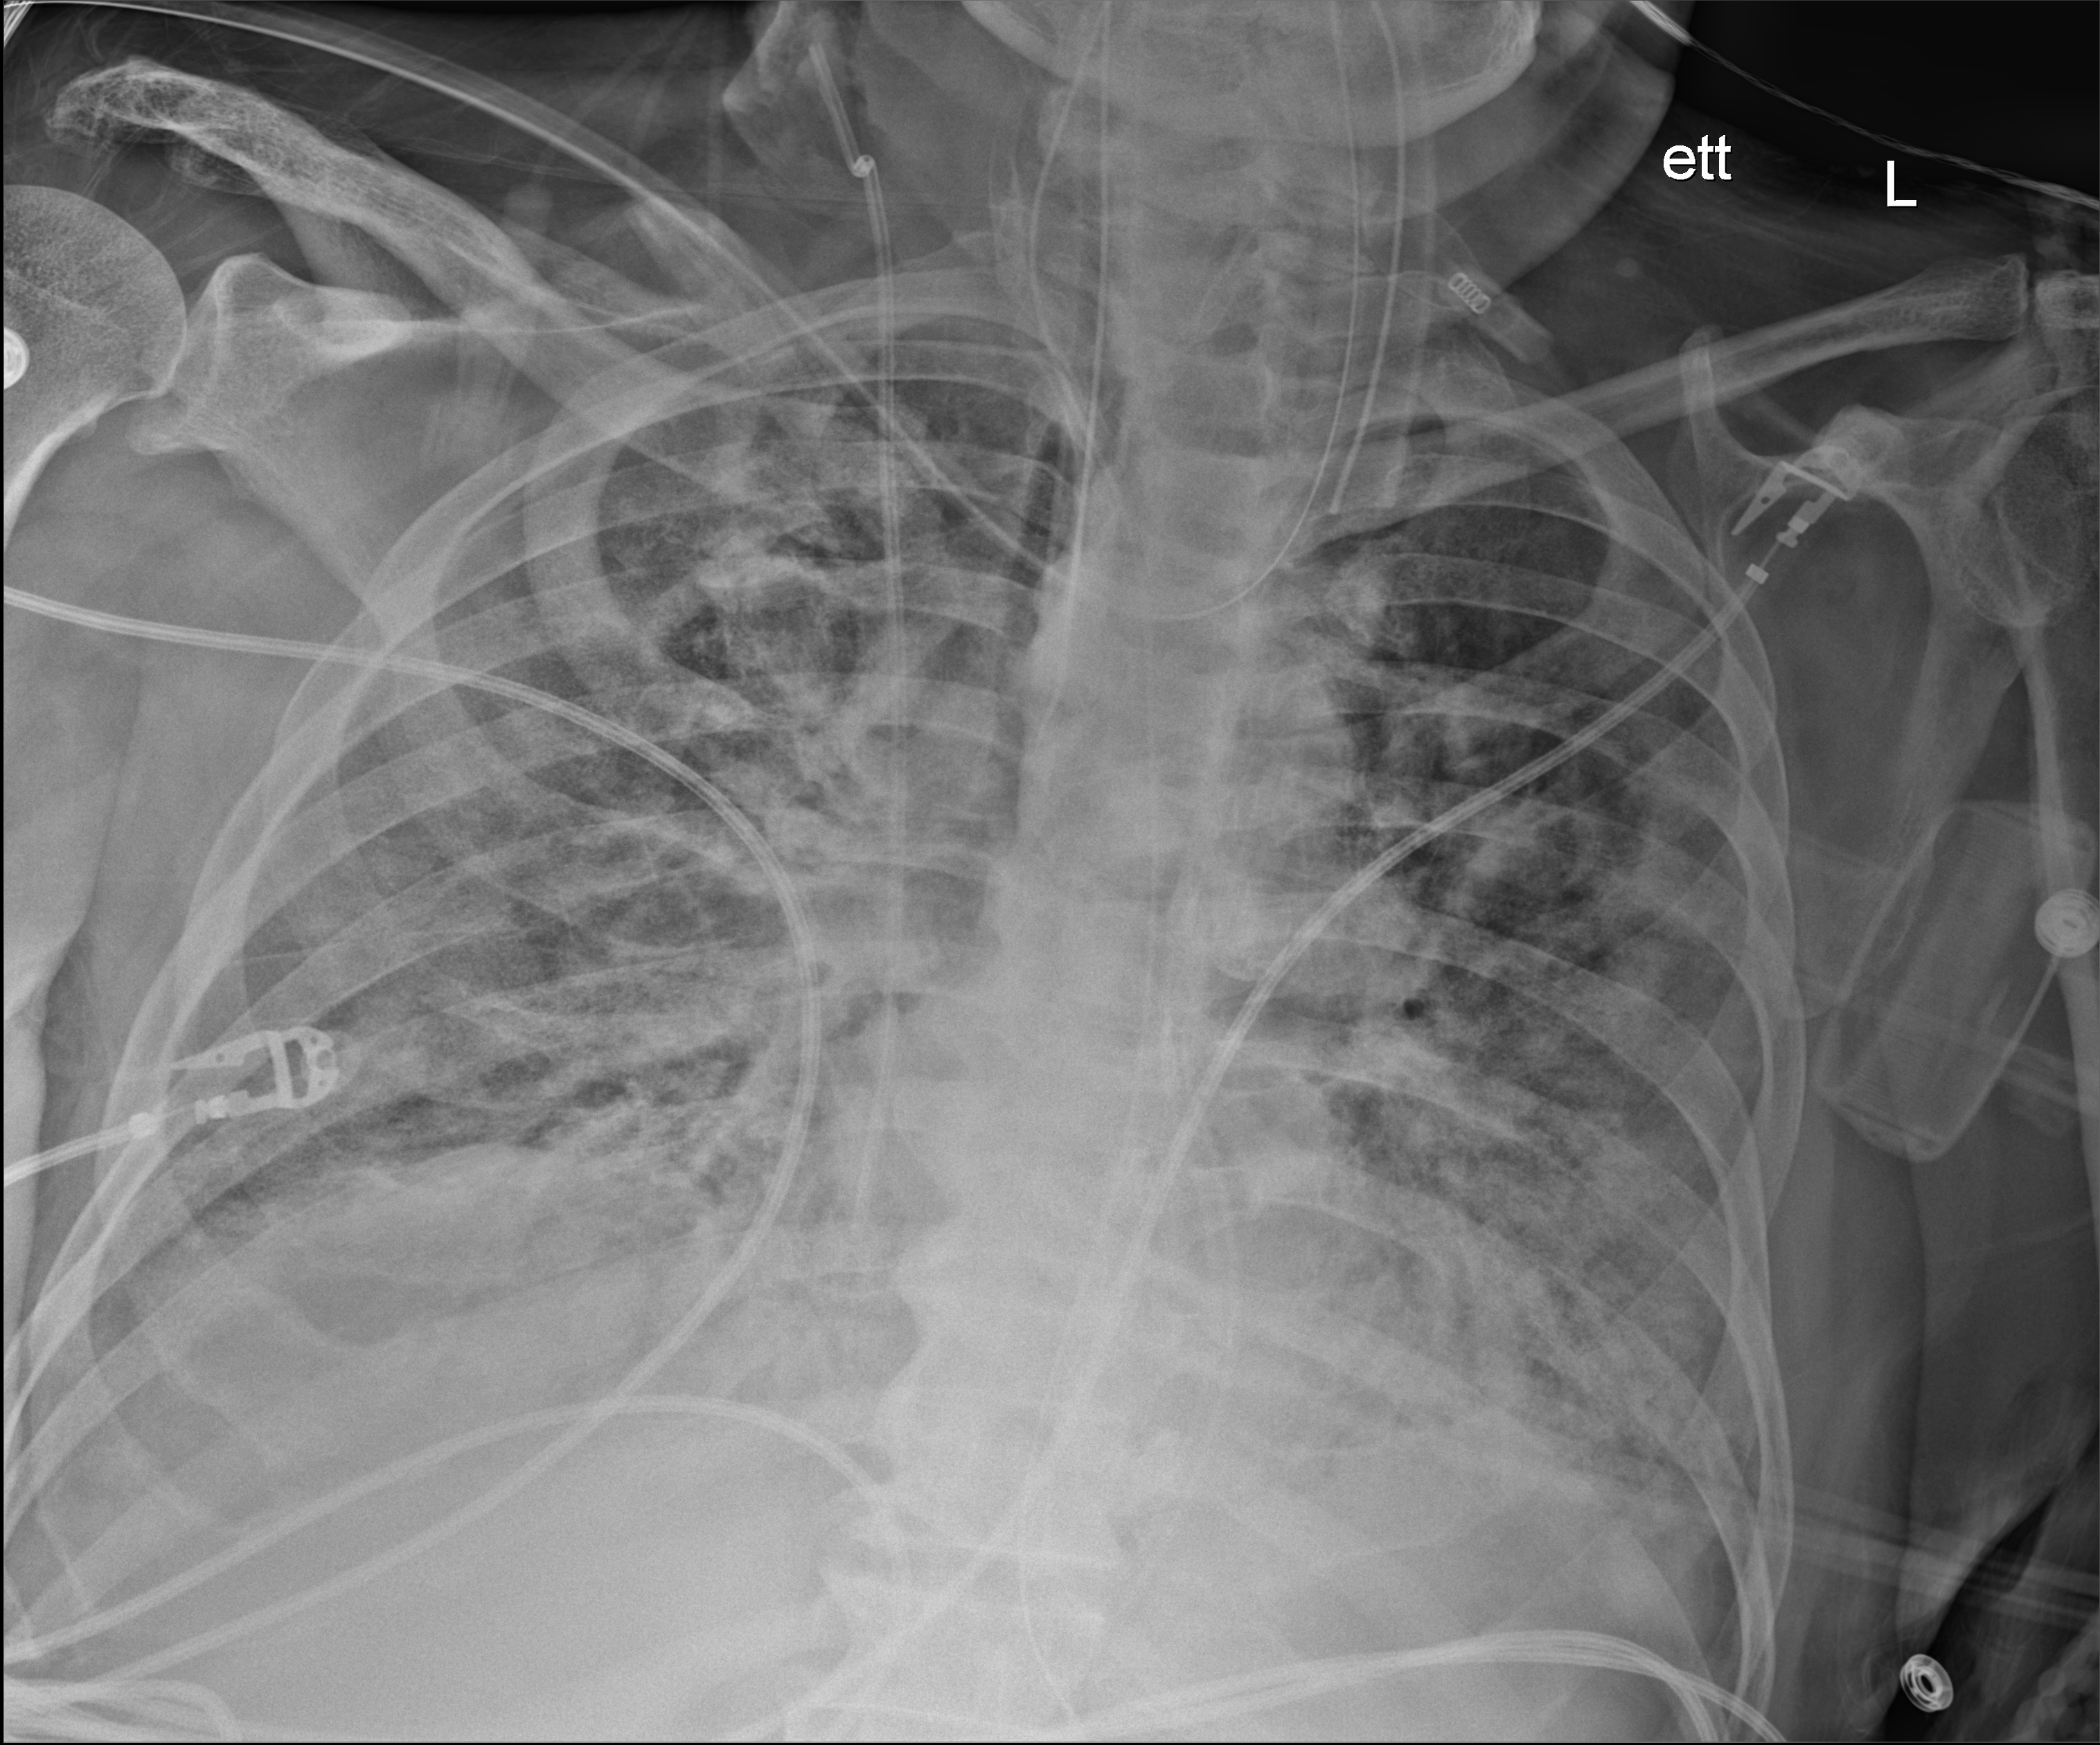
Portable chest radiograph, anteroposterior (AP) projection. Patient hospitalised with COVID-19; male, aged 75–90 years.
From the hospital-stay record, not from the radiograph (when in the stay this image was taken is not recorded): mechanically ventilated during this hospital stay: yes.